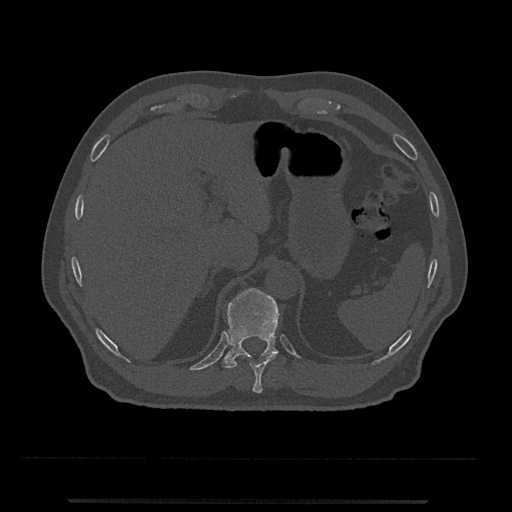
CT including the spine, one axial slice. Slice 486 of 797 in the series (ordered by position). 120 kVp. Bone window (W 1800 / L 400 HU). 0.5 mm slice thickness. 512 × 512 image matrix, field of view 419 × 419 mm. Patient: male, 63 years. From the clinical record (not read from this slice): primary cancer: prostate.
Outlined on this slice (semi-automatic segmentation, software-assisted and operator-edited):
- T10 vertebra: bounding box [x1, y1, x2, y2] px = [250, 354, 277, 393]
- T11 vertebra: [222, 288, 280, 368]